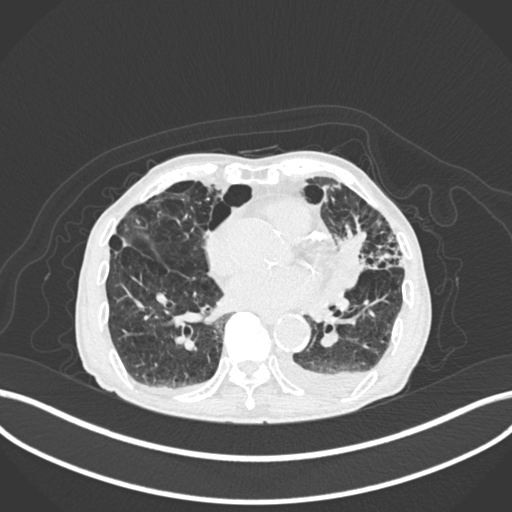
Chest CT, one axial slice; position 82 of 400 along the scan axis; reconstruction kernel B30f; 120 kVp; lung window (W 1500 / L -600 HU); 1 mm slice thickness; 512 × 512 image matrix, field of view 400 × 400 mm. Patient: male, 90 years or older. From the clinical record (not read from this slice): clinical TNM (as recorded): T2b N1 M0.
Outlined on this slice (rectangle marked by the reading radiologist):
- lung tumour (recorded histology: squamous cell carcinoma): bounding box [x1, y1, x2, y2] px = [332, 220, 372, 289]